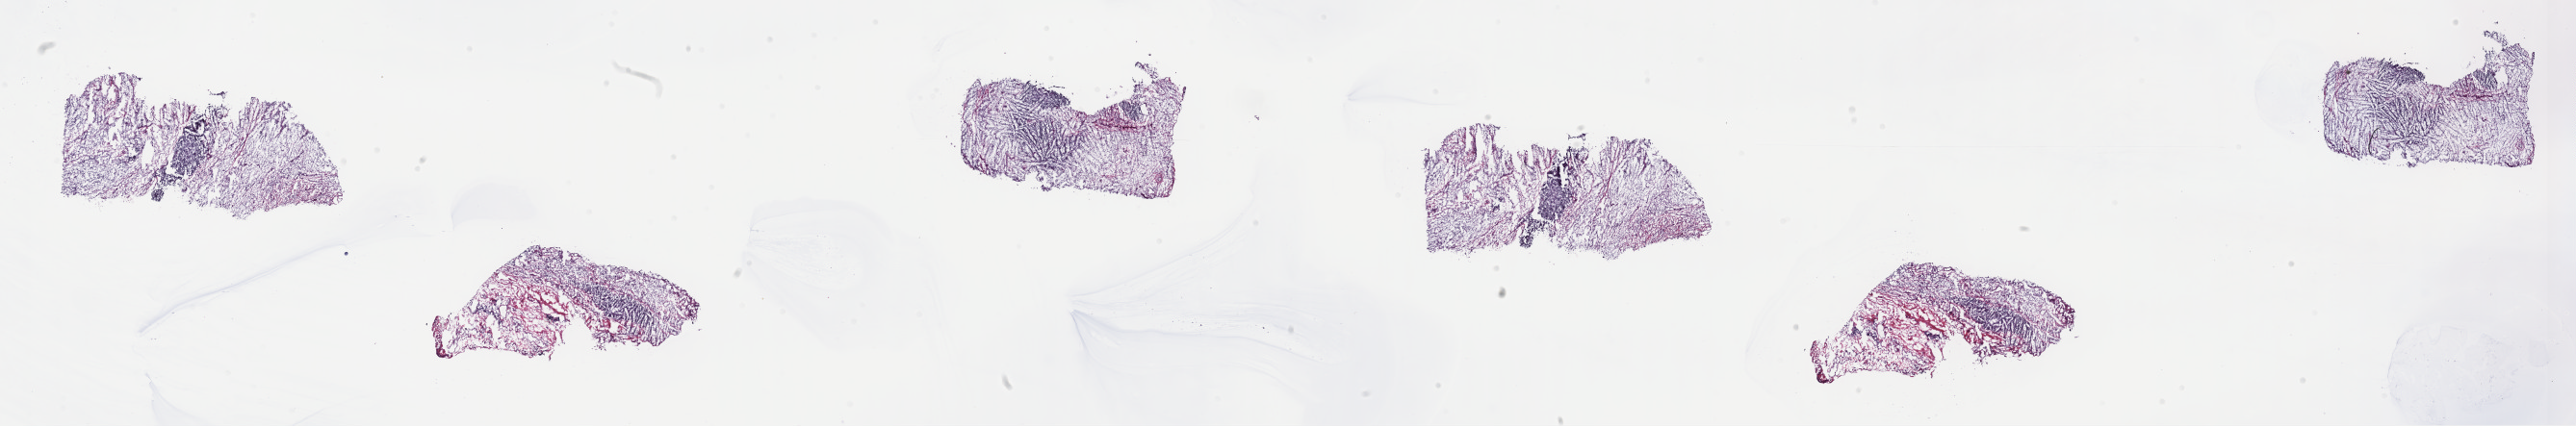
Whole-slide histology image, H&E — low-resolution overview of the scanned area, about 43.3 x 7.2 mm (slide scanned at 40x). Frozen section from the top of the tissue portion. Primary tumour sample from the connective, subcutaneous and other soft tissues. Patient: male, age at initial diagnosis 68 years. Slide review estimates, as recorded: tumour cells 100%, tumour nuclei 80%, normal cells 0%, stromal cells 0%, necrosis 0%. Inflammatory infiltration, as recorded: lymphocyte infiltration 2%, monocyte infiltration 0%, neutrophil infiltration 0%.
Pathologic diagnosis: Dedifferentiated liposarcoma (connective, subcutaneous and other soft tissues of pelvis).